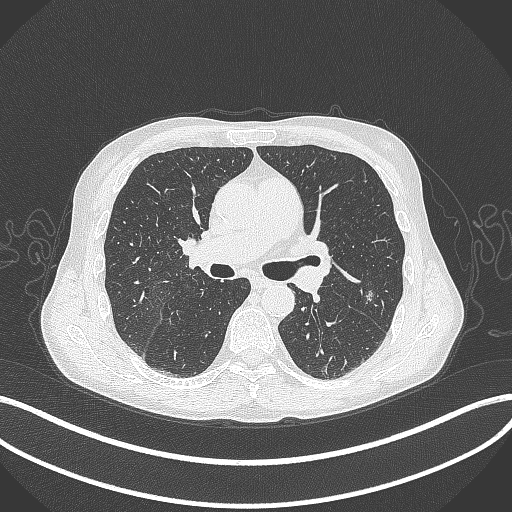
Chest CT, one axial slice; position 215 of 429 along the scan axis; reconstruction kernel B70f; 120 kVp; lung window (W 1500 / L -600 HU); 1 mm slice thickness; 512 × 512 image matrix, field of view 400 × 400 mm. Male patient, age 58 years. Case-level facts recorded for this patient, not image findings: clinical TNM (as recorded): T1c N0 M0.
Outlined on this slice (rectangle marked by the reading radiologist):
- lung tumour (recorded histology: adenocarcinoma): box from (x=364, y=289) to (x=380, y=308) px